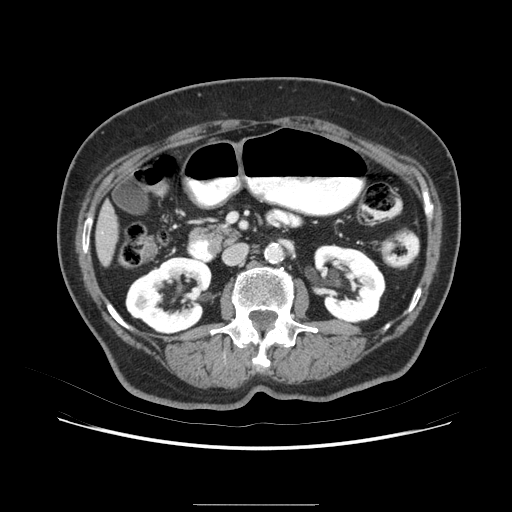
Contrast-enhanced abdominal CT (liver protocol), one axial slice. Slice 23 of 79 in the series (ordered by position). 120 kVp. Soft-tissue window (W 400 / L 40 HU). 2.5 mm slice thickness. 512 × 512 image matrix, field of view 380 × 380 mm. From the clinical record (not read from this slice): diagnosis: hepatocellular carcinoma (patient treated with transarterial chemoembolisation; whether this scan precedes or follows treatment is not stated here); TNM stage (as recorded): Stage-I.
Outlined on this slice (semi-automatic segmentation, software-assisted and operator-edited):
- liver parenchyma outside the tumour (the mass and vessels are separate outlines, so this box may not span the whole liver): bounding box (x1, y1, x2, y2) in pixels: (94, 158, 154, 286)
- liver vessels: (108, 231, 118, 248)